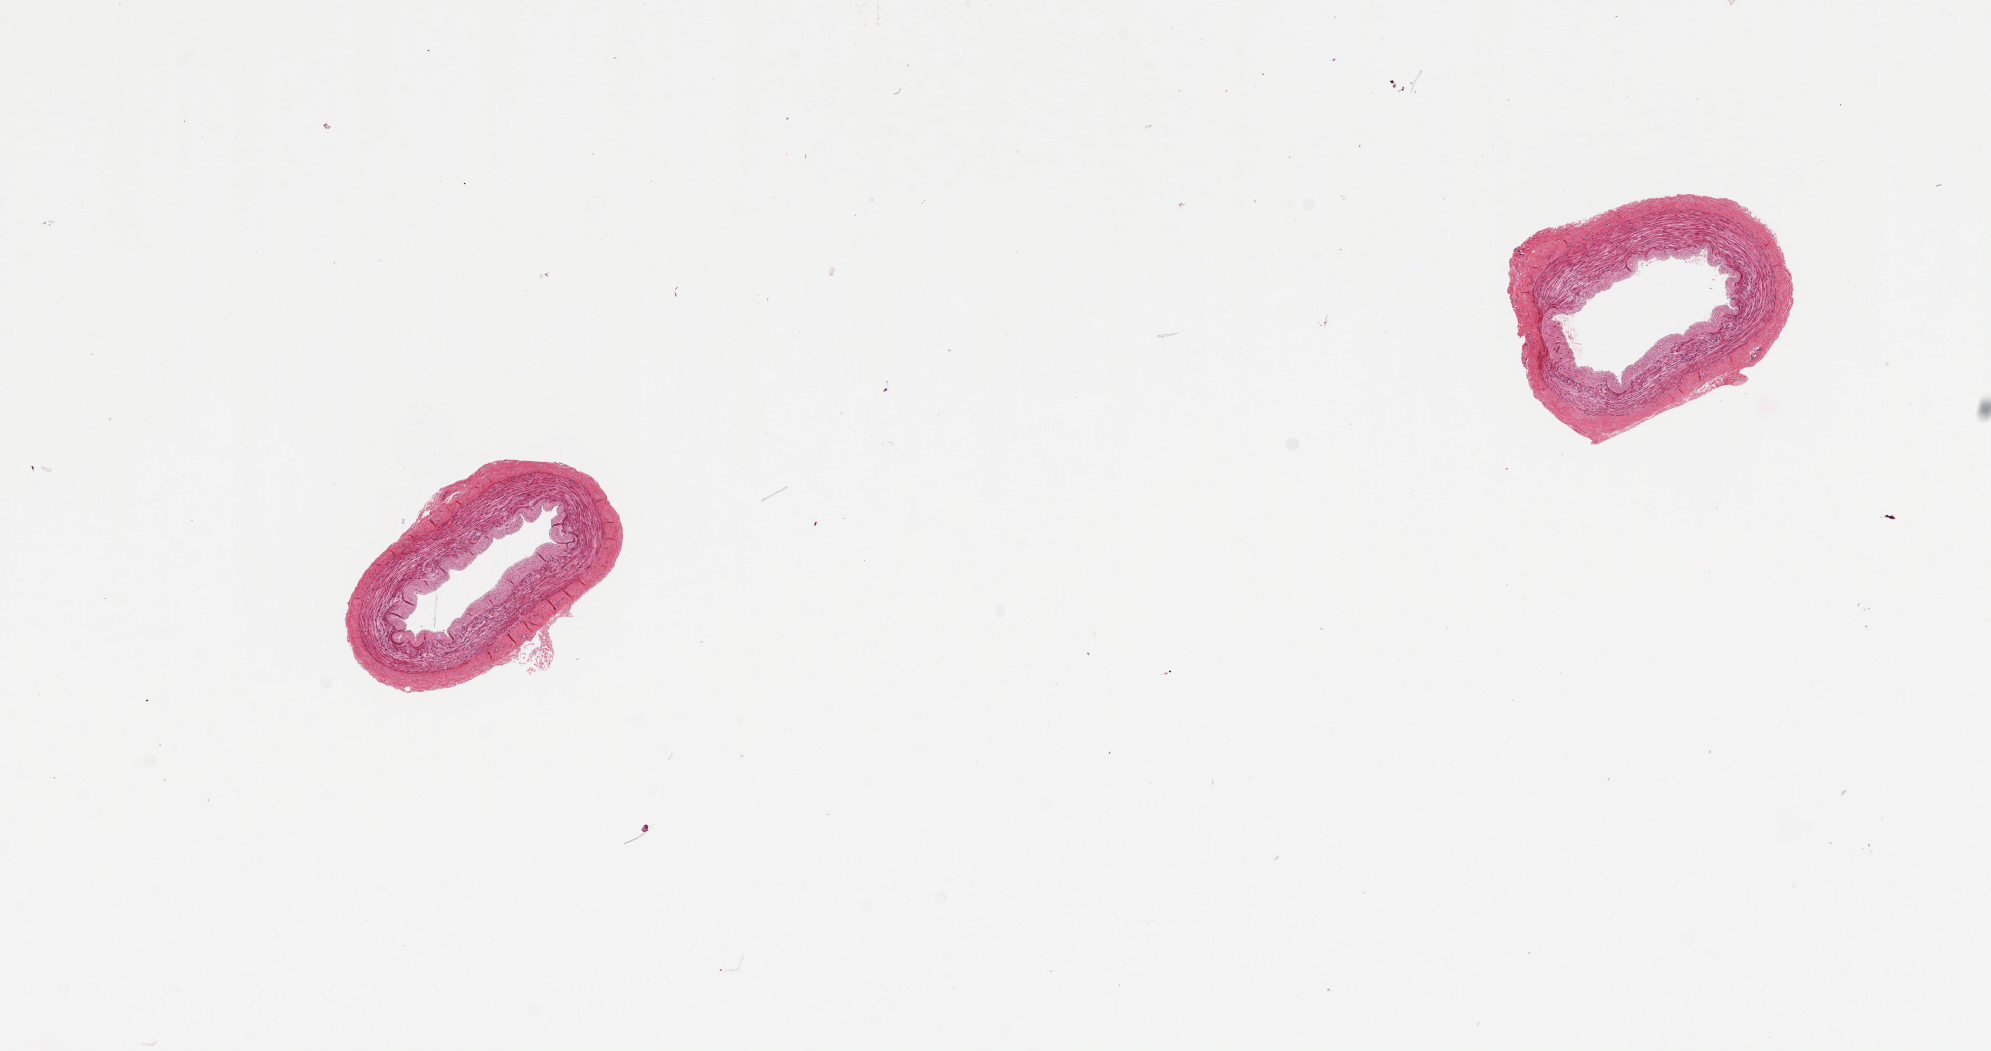
H&E whole-slide image — low-resolution overview of the scanned area, about 15.8 x 8.3 mm (acquisition: 20x scan), PAXgene-fixed, paraffin-embedded tissue, section of tibial artery (target tissue), donor tissue sample. Female donor.
• review note (as recorded): 2 pieces, well trimmed